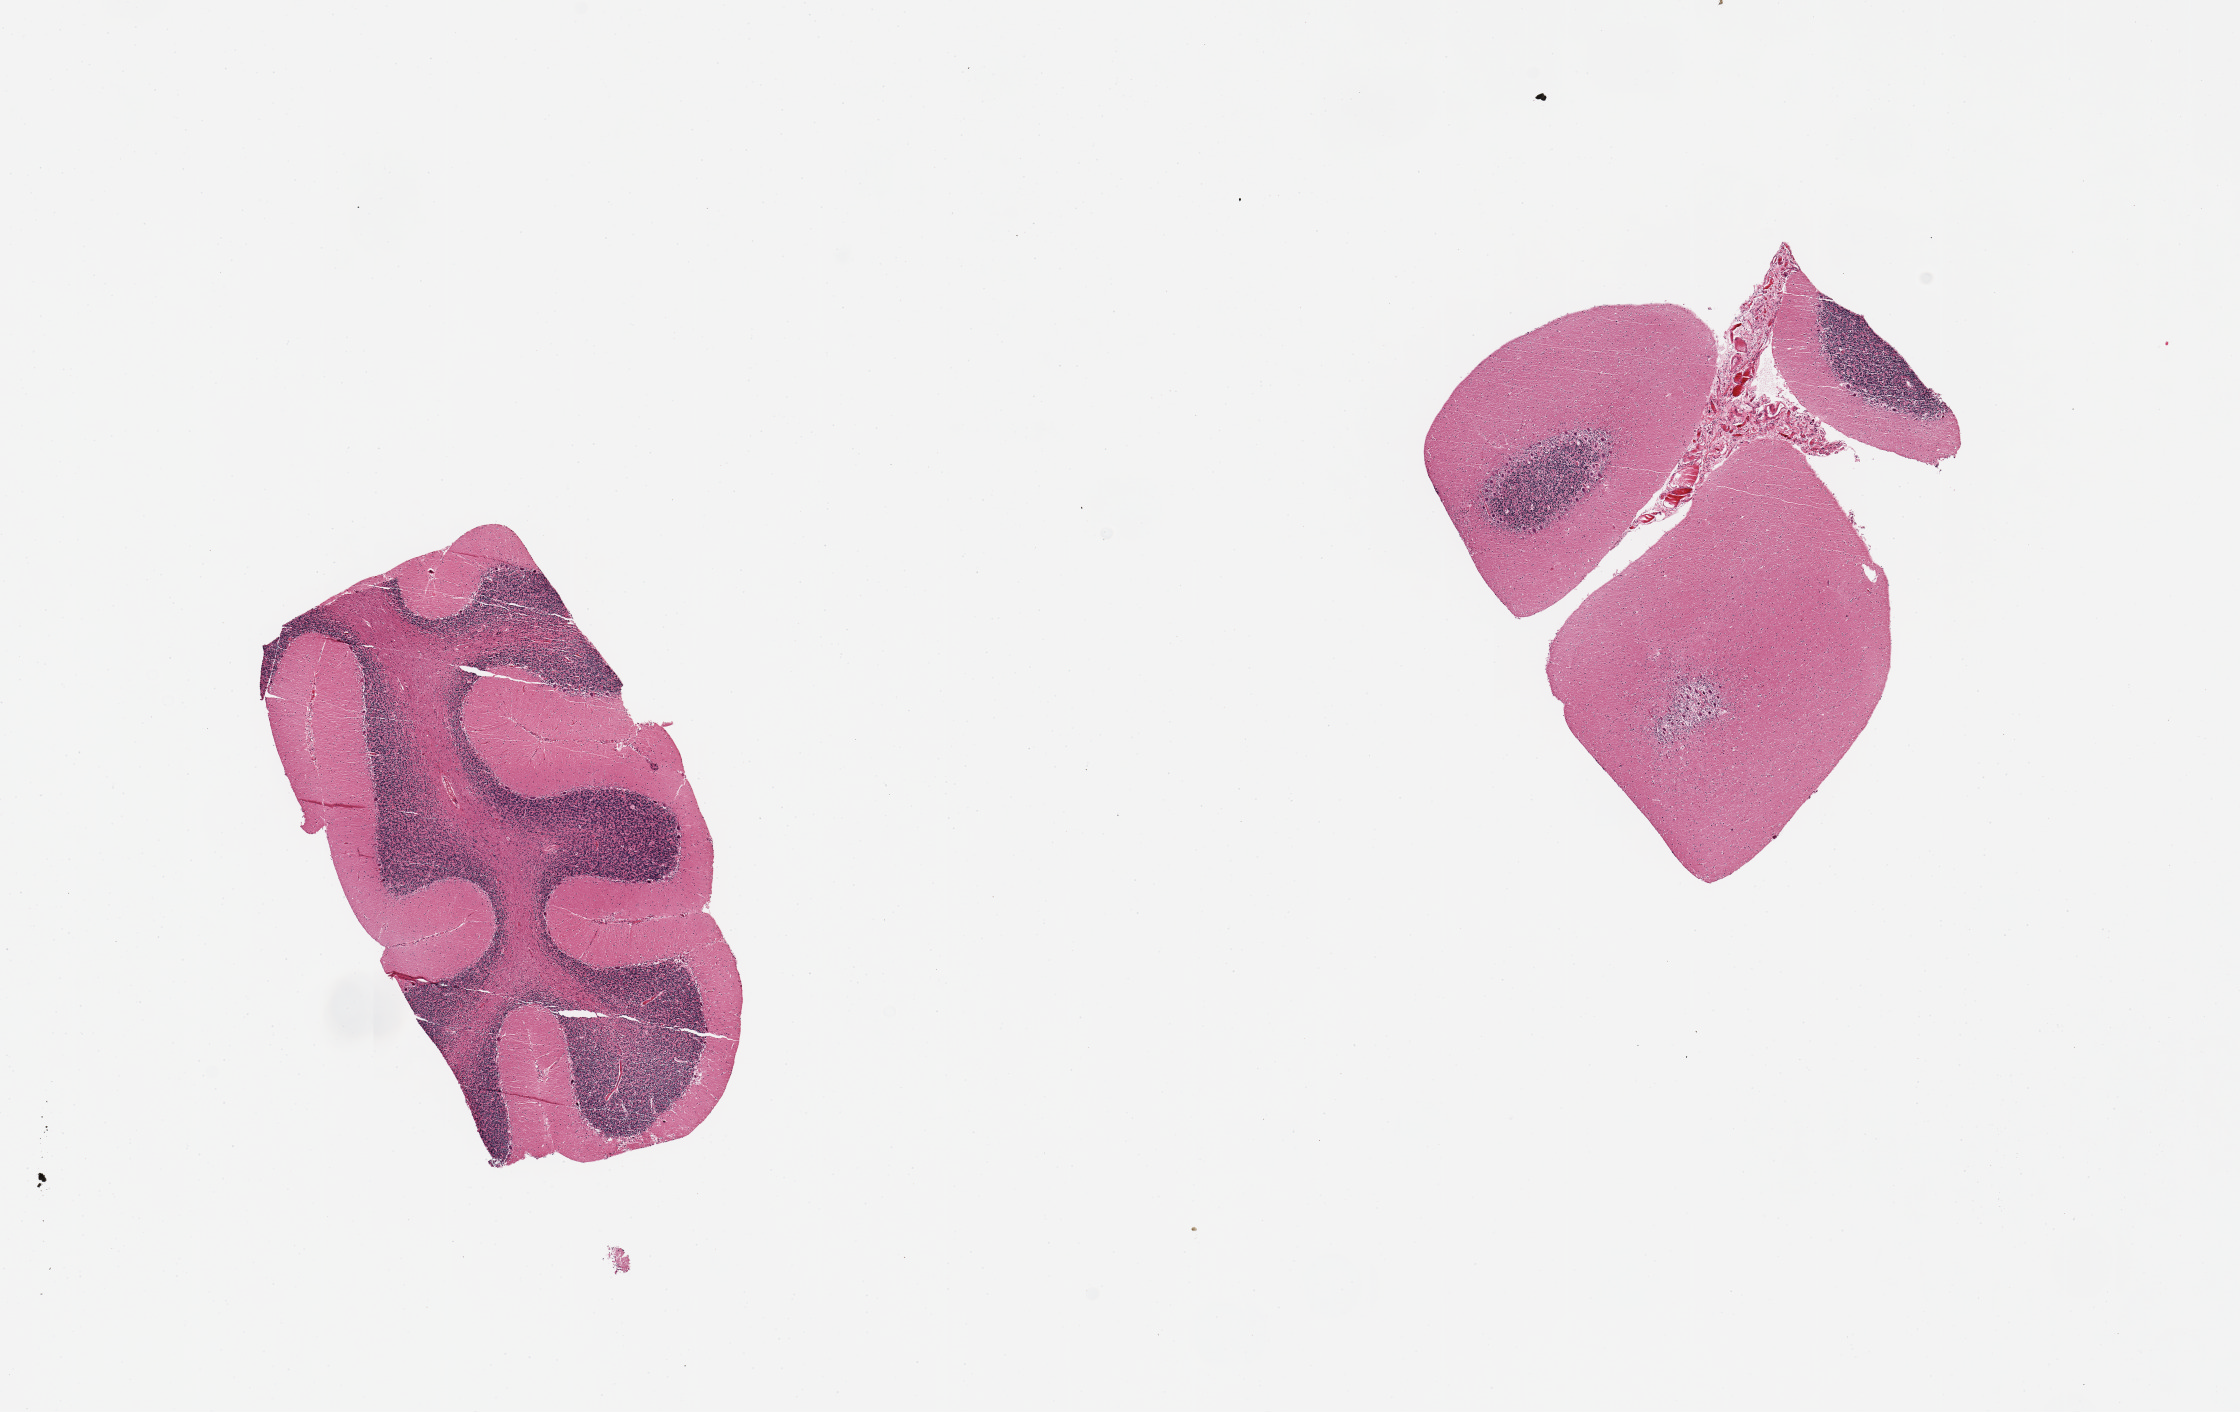
Whole-slide image, H&E stain, a low-resolution overview of the entire scanned area, about 17.7 x 11.2 mm; PAXgene-fixed paraffin-embedded (PFPE) section; section of cerebellum (target tissue); donor tissue sample. Donor sex: male.
Pathologist's review note for this sample: 2 pieces; cerebellum. Purkinje cells well visualized, small attachment of meninges.